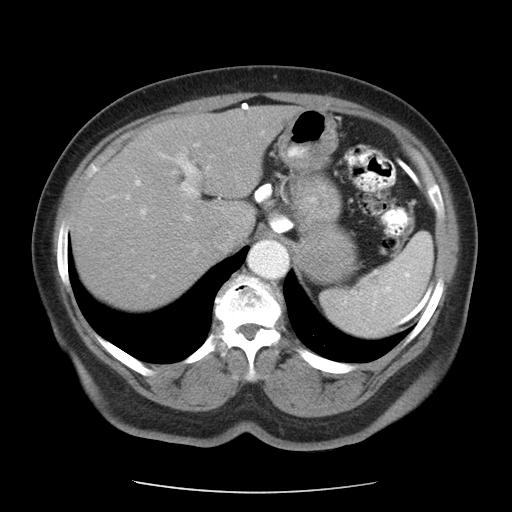
Contrast-enhanced abdominal CT, one axial slice. Slice 74 of 95 in the series (ordered by position). Reconstruction kernel STANDARD. 120 kVp. Soft-tissue window (W 400 / L 40 HU). 512 × 512 image matrix, field of view 362 × 362 mm. Patient: female, 71 years. Case-level facts recorded for this patient, not image findings: diagnosis: adrenocortical carcinoma; tumour side: left adrenal; tumour size at pathology: 8.8 cm; Ki-67 index: 20 %; stage (as recorded): 2.
Structures marked on this image (semi-automatic segmentation, software-assisted and operator-edited):
- mass: bounding box (x1, y1, x2, y2) in pixels: (295, 226, 356, 283)